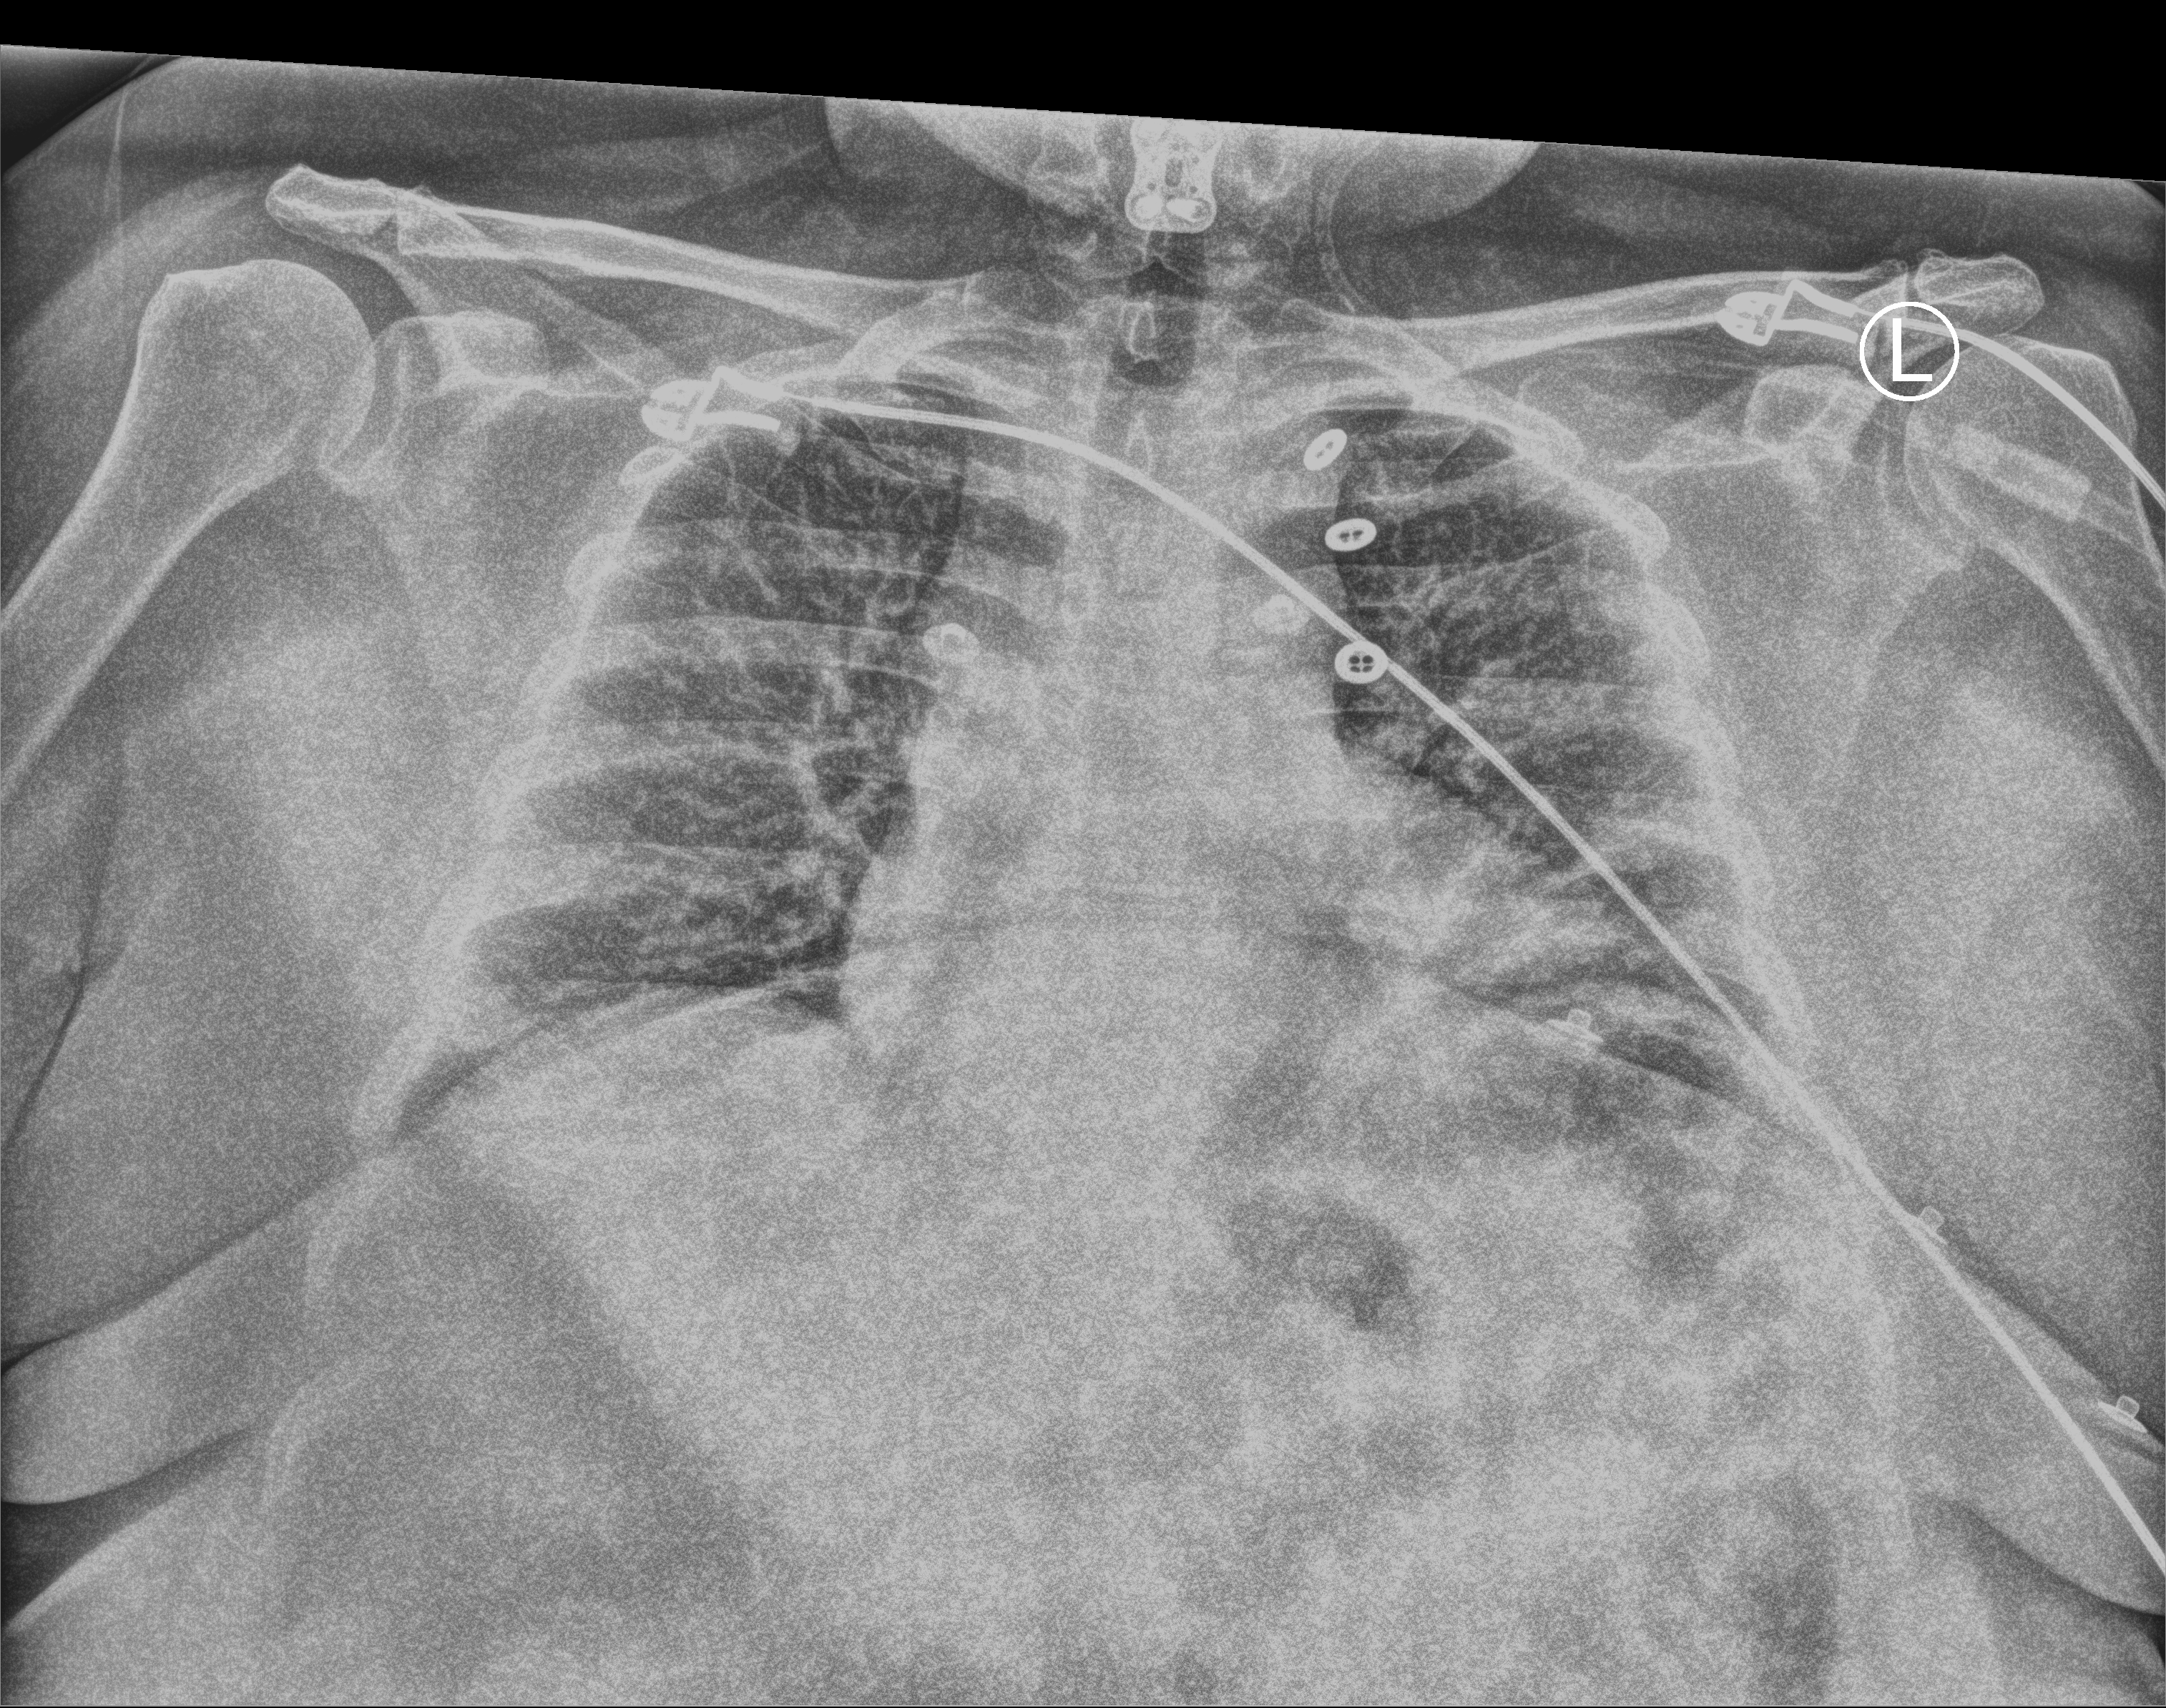
Bedside chest radiograph (computed radiography), anteroposterior (AP) projection. Patient hospitalised with COVID-19; female, aged 18–59 years.
From the hospital-stay record, not from the radiograph (when in the stay this image was taken is not recorded): admitted to intensive care during this hospital stay: no.